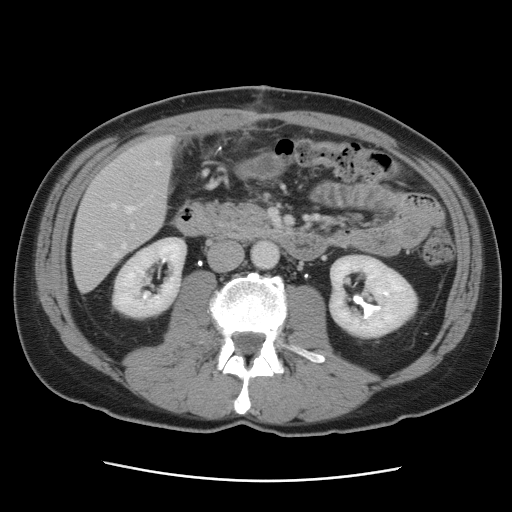
Contrast-enhanced abdominal CT, one axial slice; position 29 of 89 along the scan axis; 120 kVp; intravenous contrast given; soft-tissue window (W 400 / L 40 HU); 5 mm slice thickness; 512 × 512 image matrix, field of view 366 × 366 mm. Male patient, age 59 years. From the clinical record (not read from this slice): diagnosis: colorectal cancer liver metastases, imaged before liver resection; multiple liver metastases: yes; largest metastasis: 0.6 cm; disease in both lobes: yes.
Structures marked on this image (manually delineated by an expert):
- hepatic veins: box from (x=98, y=162) to (x=160, y=258) px
- liver: (x=73, y=138)–(x=173, y=290)
- planned liver remnant (the part of the liver to remain after resection): (x=74, y=138)–(x=174, y=246)
- portal vein (with intrahepatic branches): (x=131, y=224)–(x=134, y=228)